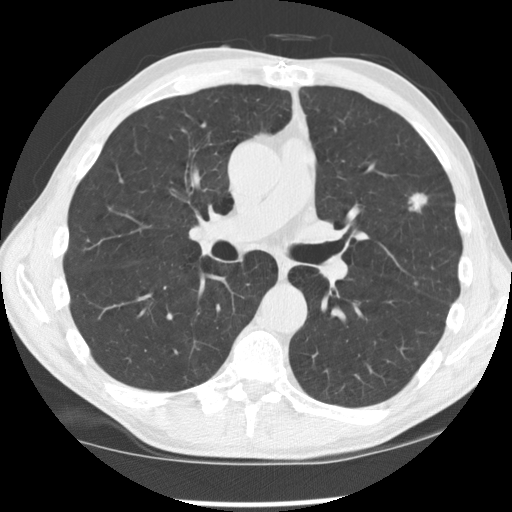
Chest CT (low-dose screening protocol), one axial image. Second annual screen. Lung window (W 1500 / L -600 HU). 2.5 mm slice thickness. Standard (soft-tissue) reconstruction kernel (STANDARD). Slice 73 of 170 in the series. Male participant, aged 64 years at enrolment. Current smoker at enrolment.
Expert-annotated lung lesion, box from (x=388, y=178) to (x=443, y=223) px. Screening reader's record for this exam (one nodule recorded; not confirmed to be the boxed lesion): non-calcified nodule or mass ≥4 mm, left upper lobe, 16 × 11 mm, spiculated (stellate) margins, soft tissue attenuation, pre-existing on the prior screen: yes; interval growth: yes. Later outcome: lung cancer diagnosed 59 days after this screen — adenocarcinoma, NOS, left upper lobe, poorly differentiated (G3), stage IA (AJCC 6th edition), 10 mm at pathology.